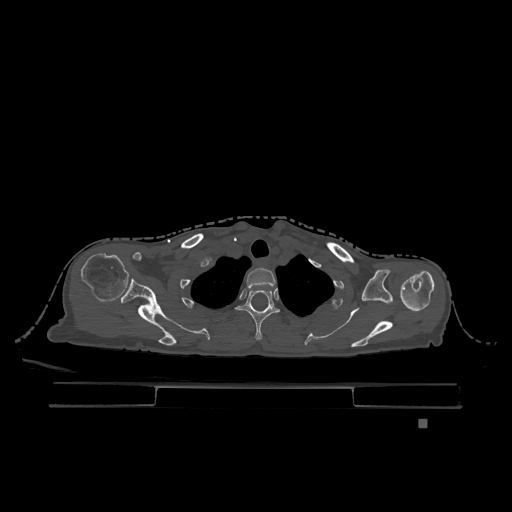
CT including the spine, one axial slice. Slice 967 of 1317 in the series (ordered by position). Bone window (W 1800 / L 400 HU). 0.5 mm slice thickness. 512 × 512 image matrix, field of view 500 × 500 mm. Female patient, age 74 years. Case-level facts recorded for this patient, not image findings: primary cancer: lung.
Structures marked on this image (semi-automatically segmented with operator editing):
- T1 vertebra: bounding box [x1, y1, x2, y2] px = [246, 268, 276, 289]
- T2 vertebra: [236, 290, 280, 340]